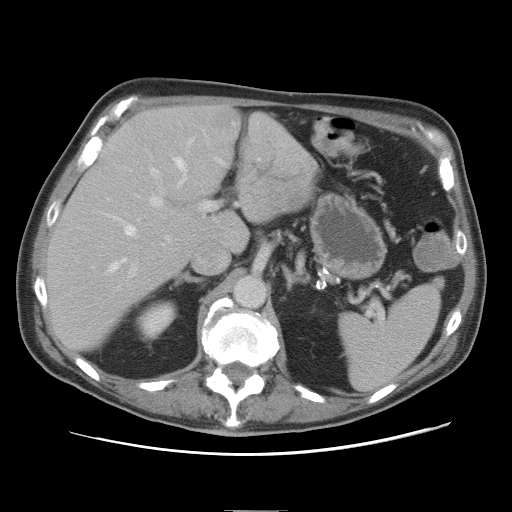
Contrast-enhanced abdominal CT, one axial slice; position 49 of 89 along the scan axis; 120 kVp; intravenous contrast given; soft-tissue window (W 400 / L 40 HU); 5 mm slice thickness; 512 × 512 image matrix, field of view 375 × 375 mm. Male patient, age 69 years. Case-level facts recorded for this patient, not image findings: diagnosis: colorectal cancer liver metastases, imaged before liver resection; multiple liver metastases: no; largest metastasis: 8.5 cm; chemotherapy before resection: no.
Annotated regions visible in this slice (outlined manually by an expert reader):
- hepatic veins: box from (x=110, y=140) to (x=193, y=271) px
- liver: (x=47, y=106)–(x=318, y=348)
- planned liver remnant (the part of the liver to remain after resection): (x=47, y=106)–(x=246, y=347)
- portal vein (with intrahepatic branches): (x=129, y=158)–(x=223, y=276)